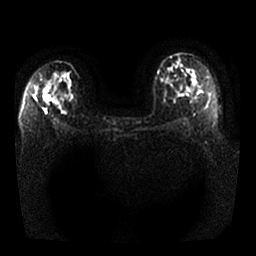
Breast MRI, one axial slice; diffusion-weighted series; image 2 of 4 stored at this slice position (different b-values; order by instance number); 1.5 T; 4 mm slice thickness; 256 × 256 image matrix. Female patient.
Outlined on this slice (manually delineated by an expert):
- tumour on diffusion-weighted imaging: bounding box <40,86,52,101> (left, top, right, bottom; pixels)